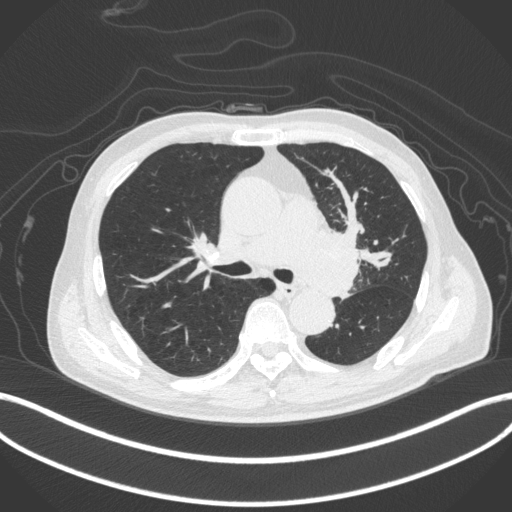
Chest CT, one axial slice; slice 269 of 420 in the series (ordered by position); reconstruction kernel B31f; lung window (W 1500 / L -600 HU); 1 mm slice thickness; 512 × 512 image matrix, field of view 400 × 400 mm. Patient: male, 77 years. From the clinical record (not read from this slice): clinical TNM (as recorded): T3 N1 M0.
Outlined on this slice (rectangle marked by the reading radiologist):
- lung tumour (recorded histology: adenocarcinoma): bounding box (x1, y1, x2, y2) in pixels: (297, 220, 364, 300)